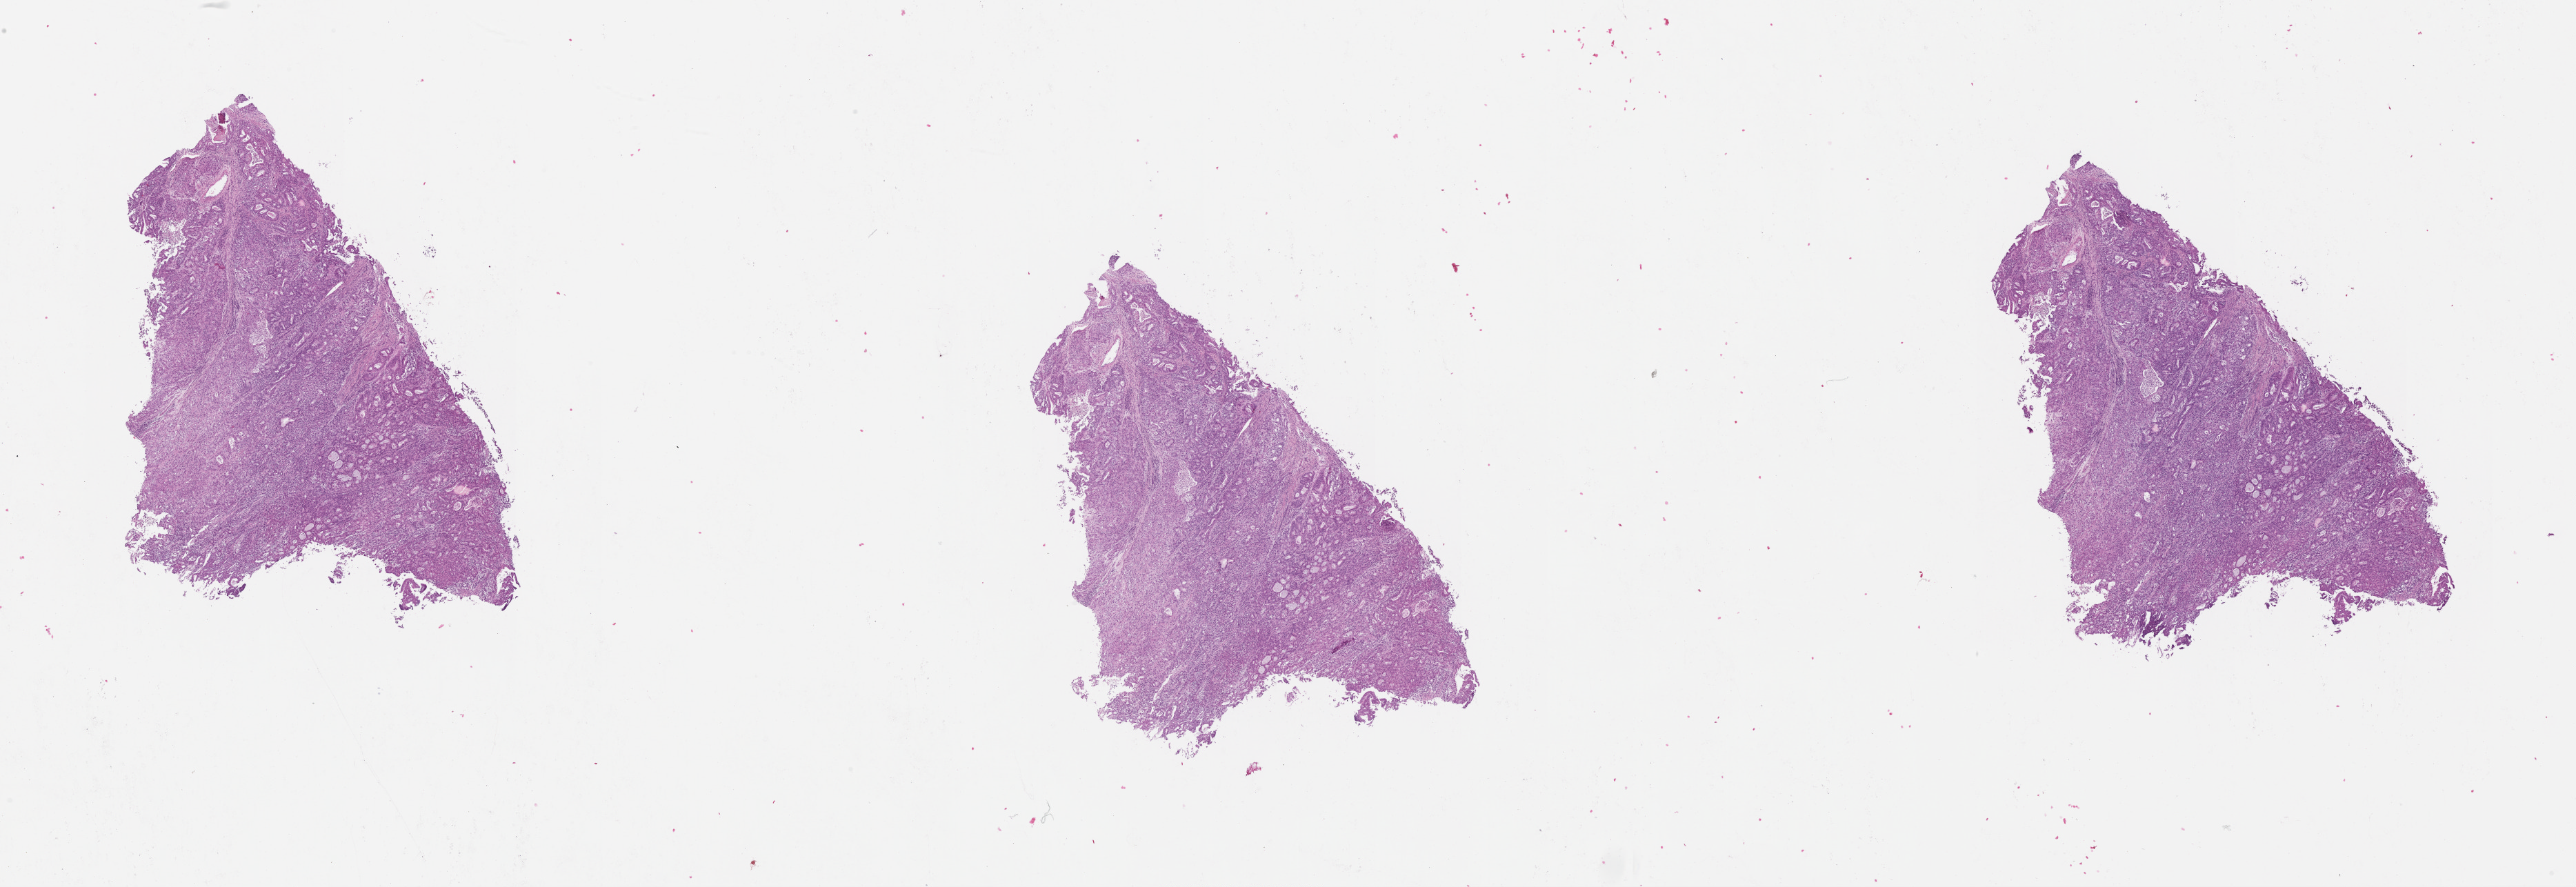
Hematoxylin and eosin (H&E) stained whole-slide image — a low-resolution overview of the entire scanned area, about 30.1 x 10.4 mm (acquisition: 20x scan). Tumour tissue sample, sampled site: uterus. Patient: female, aged 90 or older. Histologic grade: G2 (moderately differentiated). Composition of this section per pathologist review: tumour nuclei 80%, necrosis 0%.
Primary tumour site (as recorded): posterior endometrium. AJCC pathologic stage: I. Histologic diagnosis: Endometrioid adenocarcinoma, NOS.